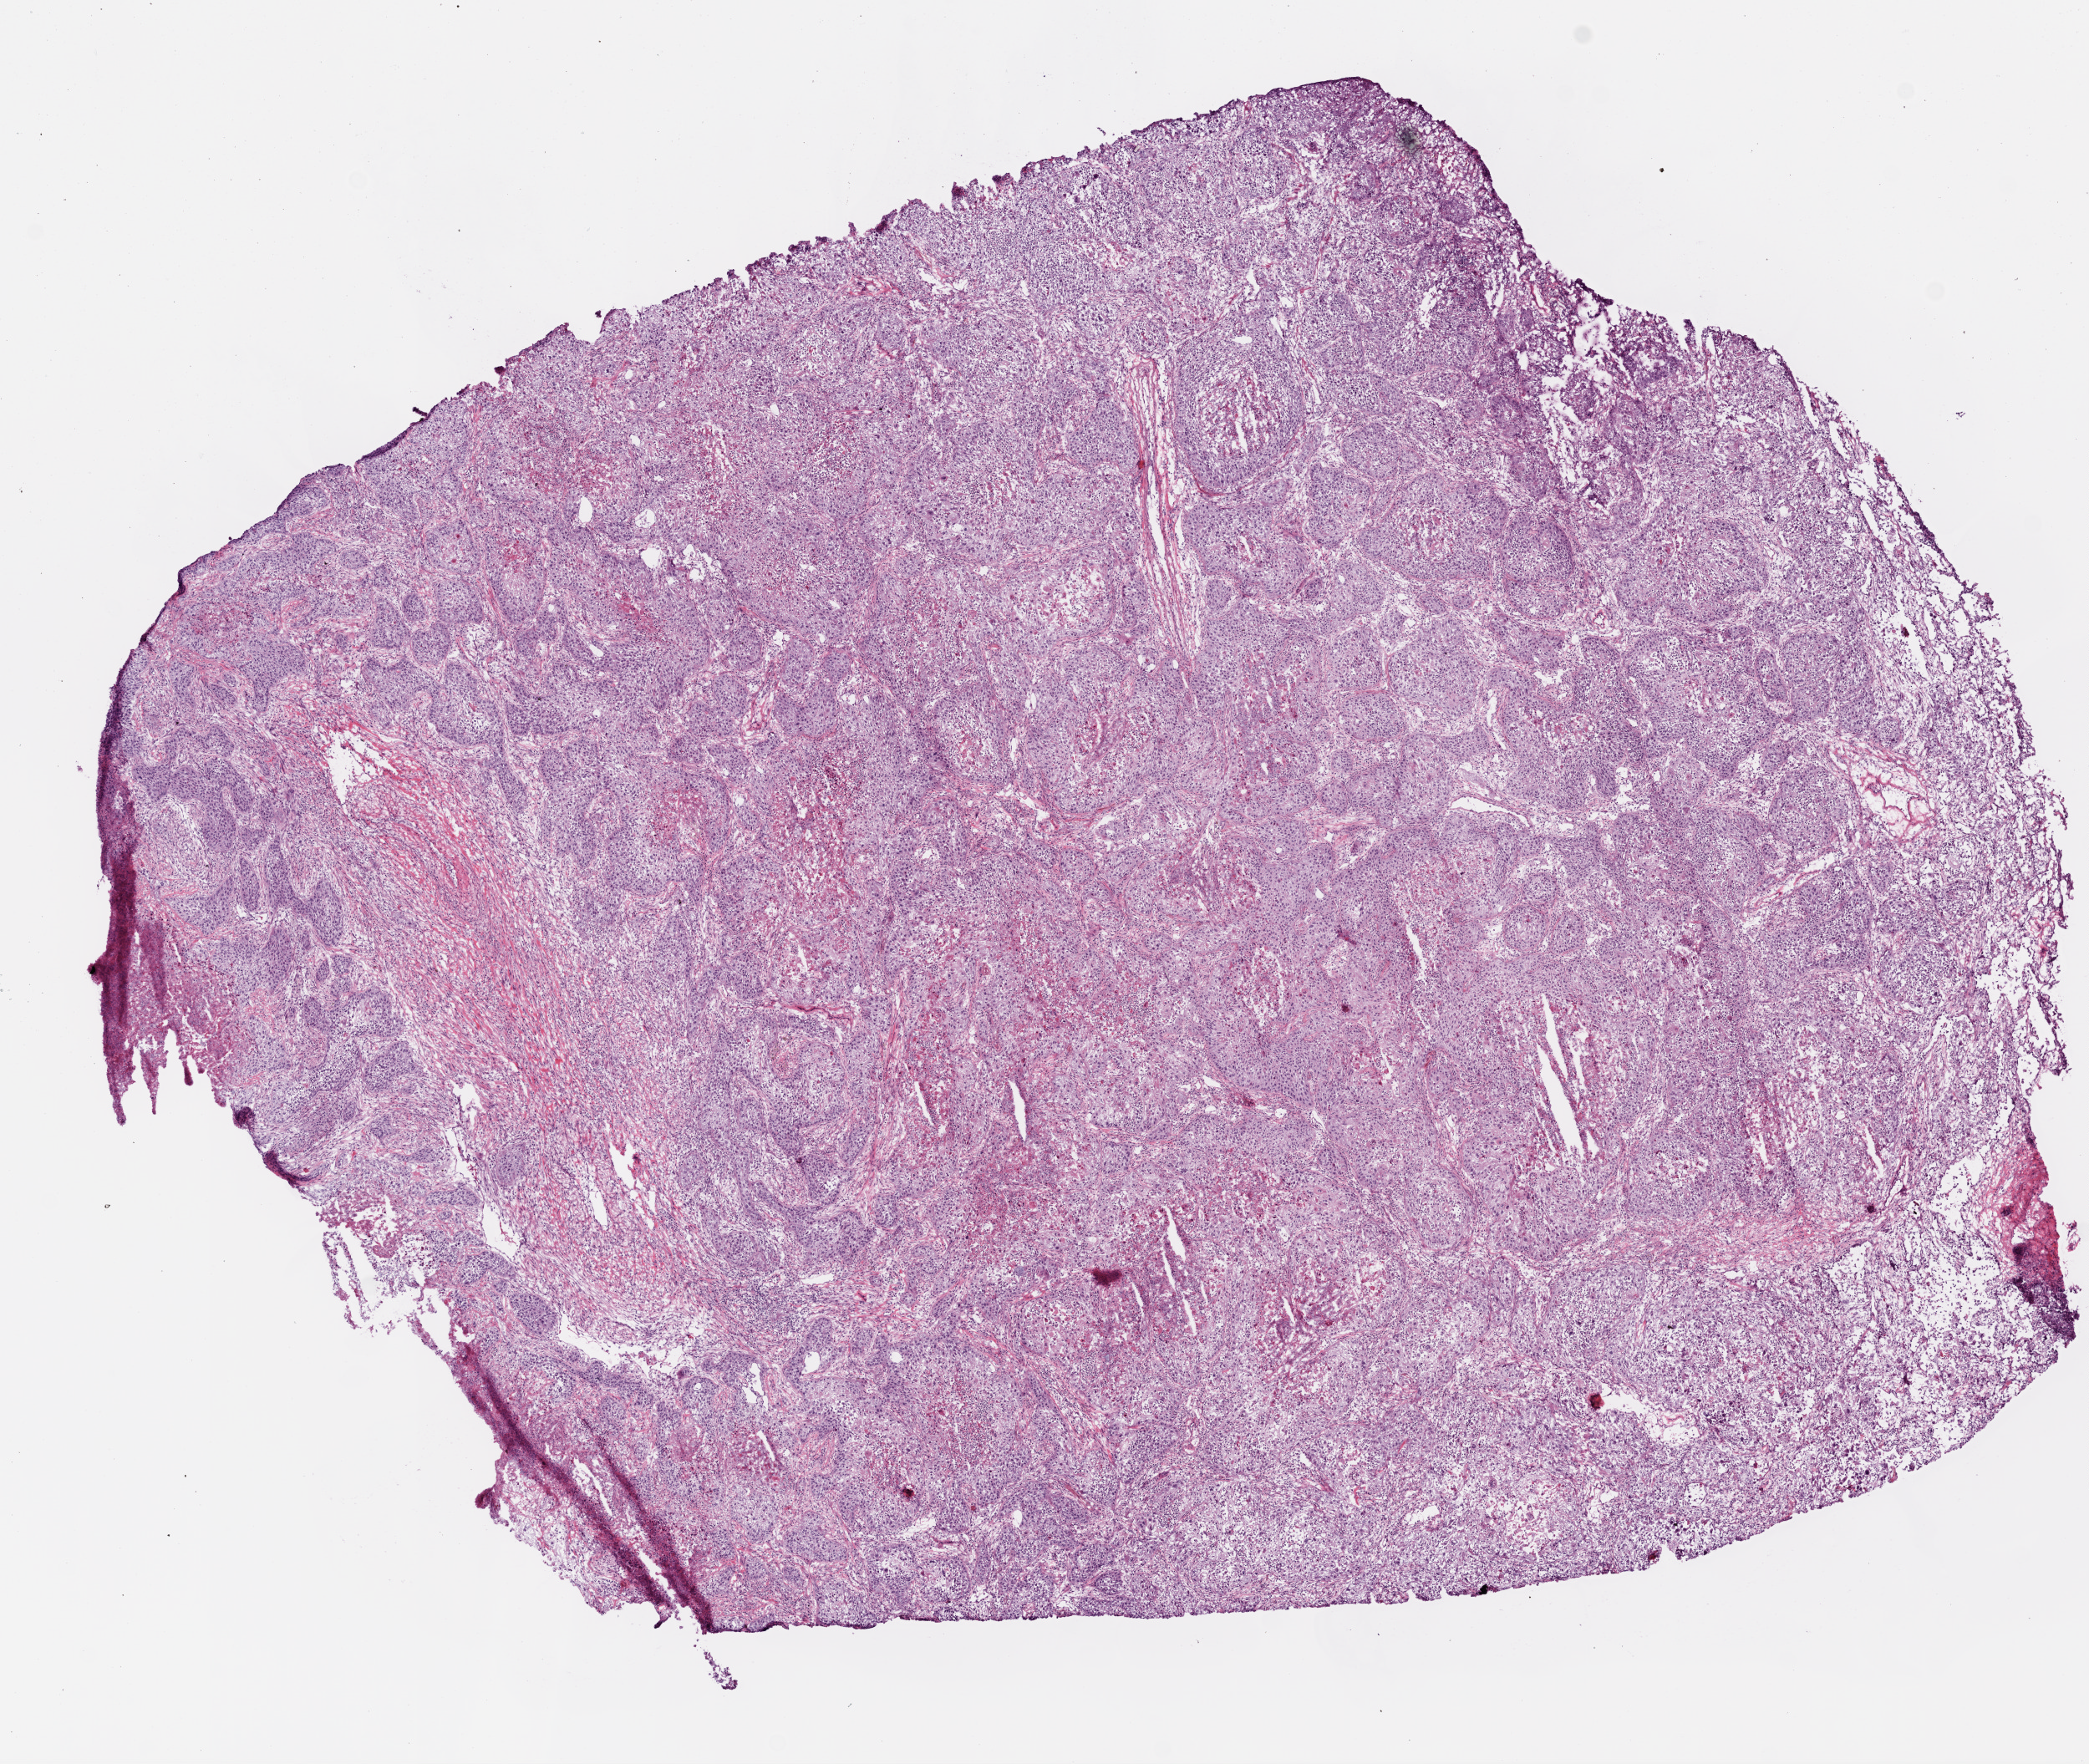
Digitized H&E tissue section (whole slide), whole scanned area (about 10.0 x 8.5 mm, acquisition: 20x scan) shown as a low-resolution overview. Frozen section from the top of the tissue portion. Lung, primary tumour sample. Female, age 62 years at initial diagnosis. Slide review estimates, as recorded: tumour cells 75%, tumour nuclei 70%, normal cells 0%, stromal cells 10%, necrosis 15%. Infiltration values recorded for this section: lymphocyte infiltration 10%.
Pathologic diagnosis: Squamous cell carcinoma, NOS (lower lobe, lung). AJCC pathologic stage: IB (5th edition). TNM: T2 N0 M0.